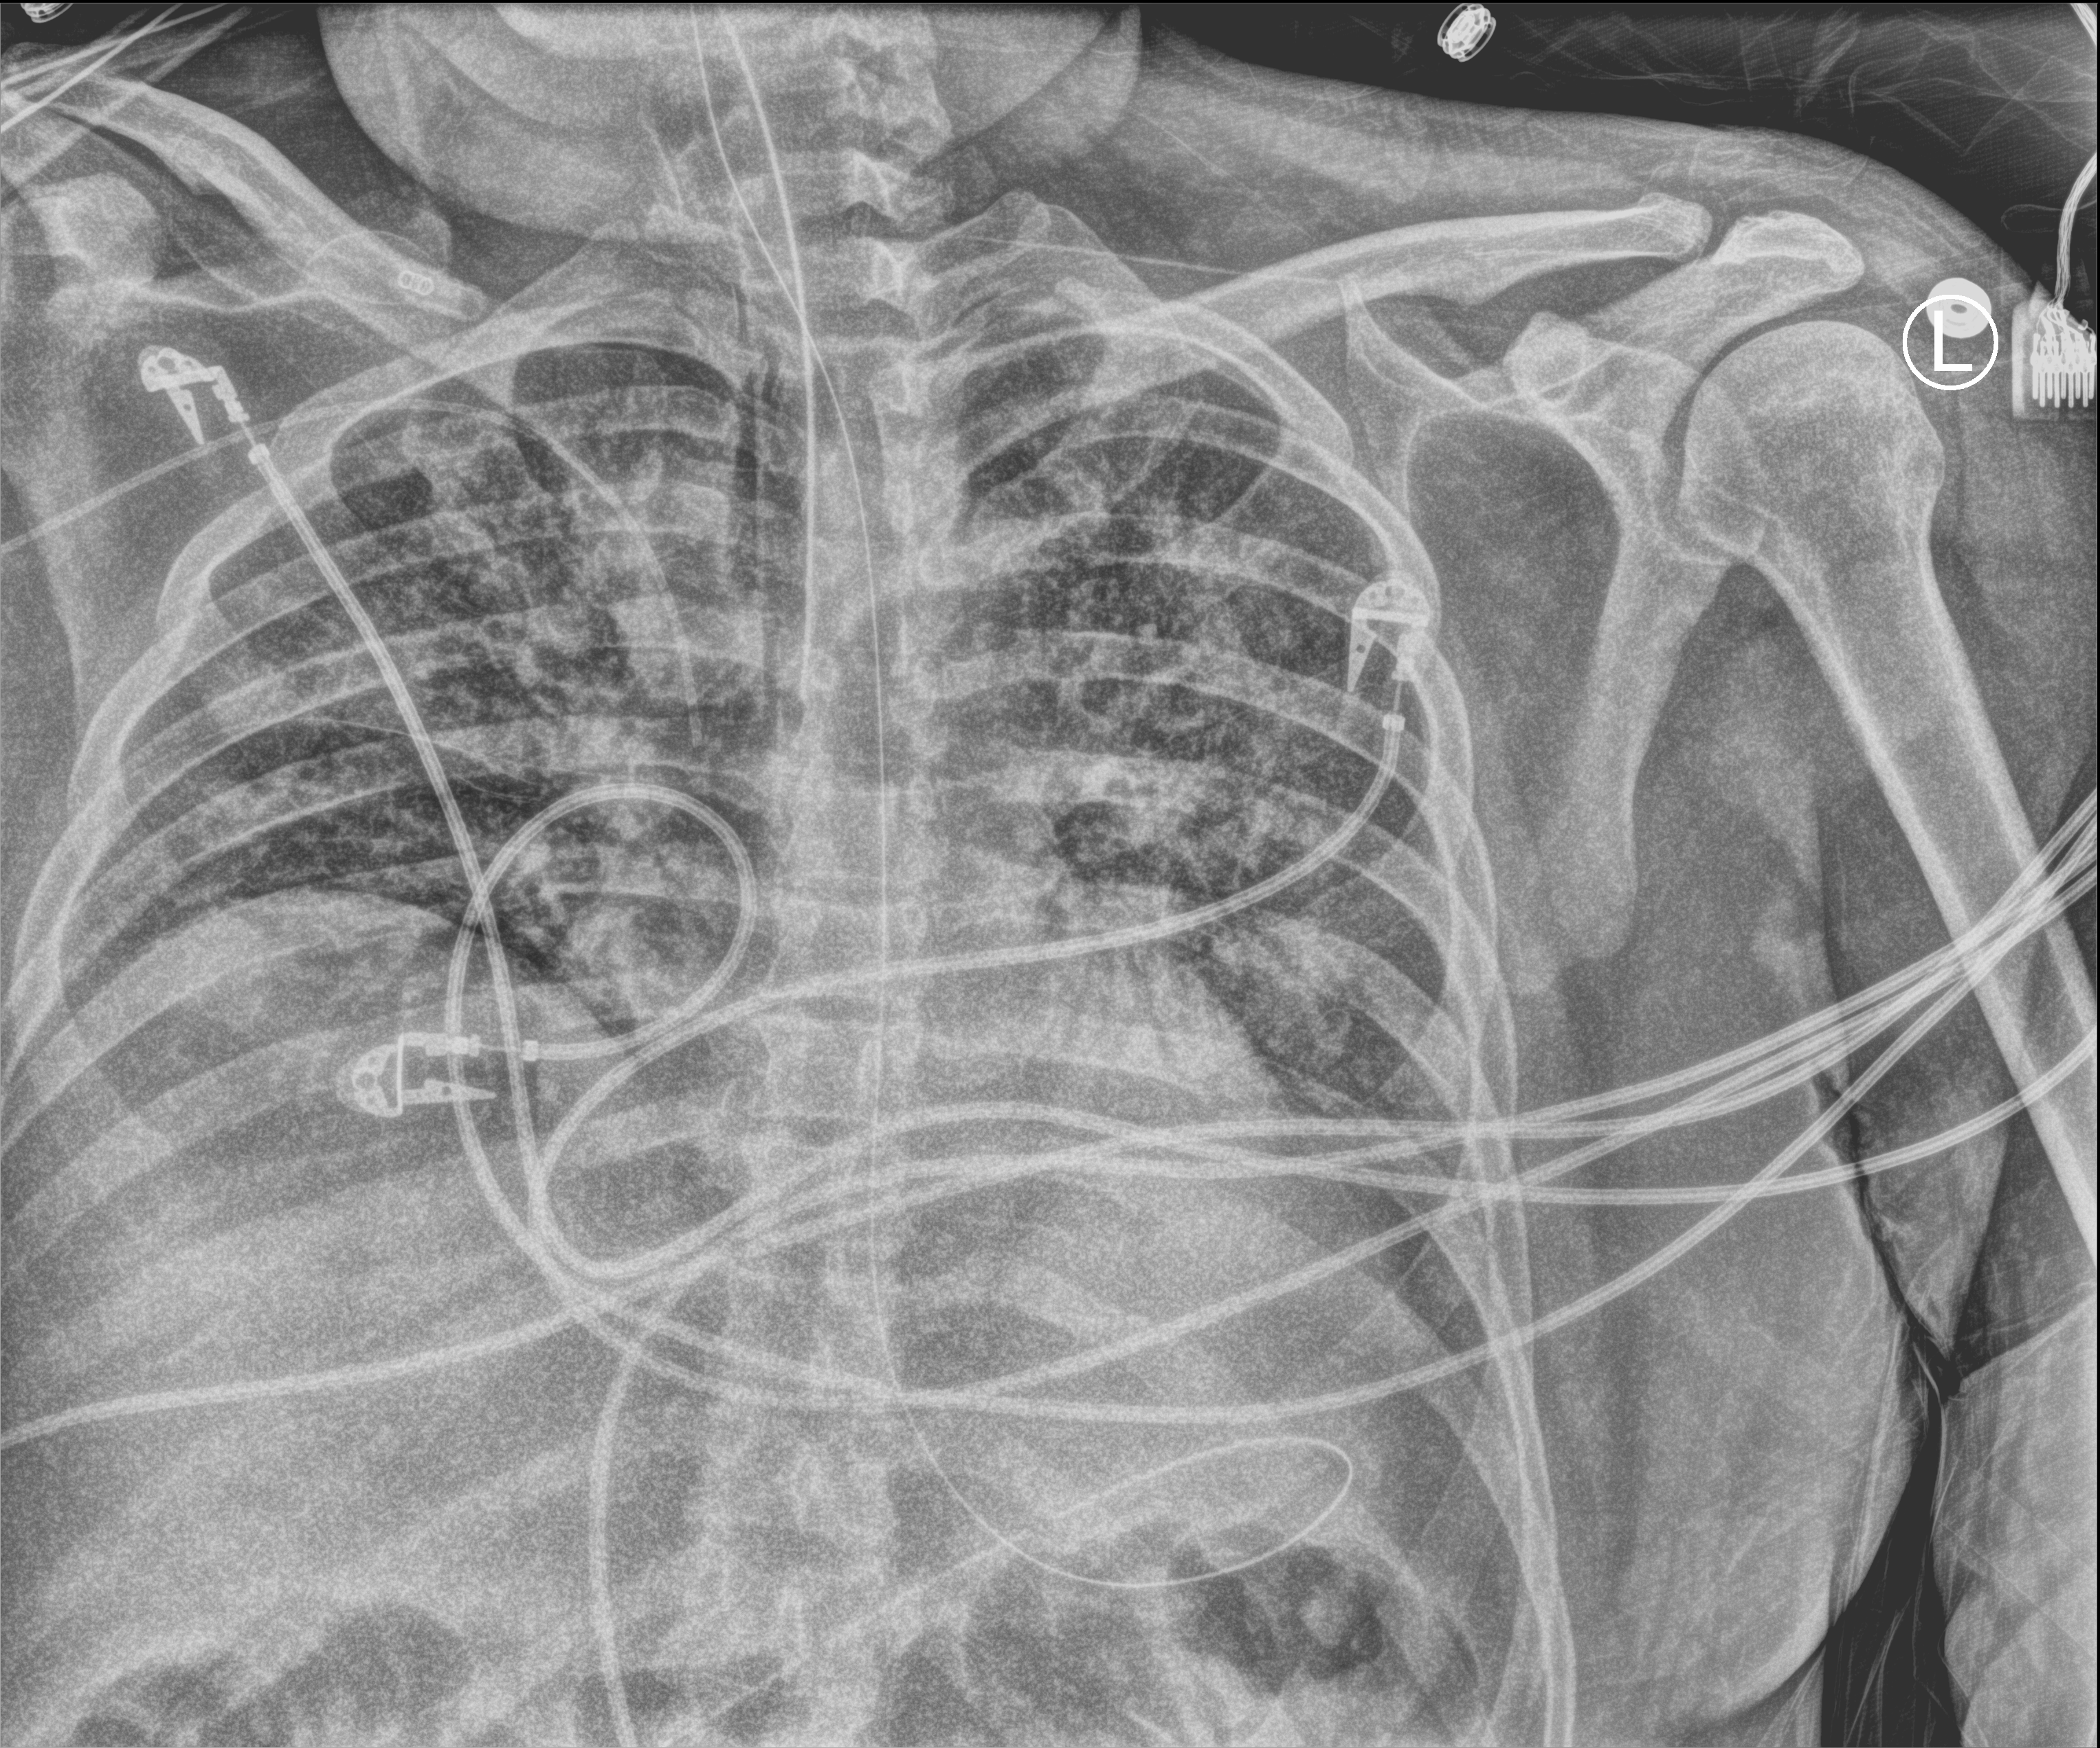
Chest X-ray (portable); anteroposterior (AP) projection. Patient hospitalised with COVID-19; male, aged 18–59 years.
From the hospital-stay record, not from the radiograph (when in the stay this image was taken is not recorded): hypertension (admission record): no; other chronic lung disease (admission record): no; admitted to intensive care during this hospital stay: yes.